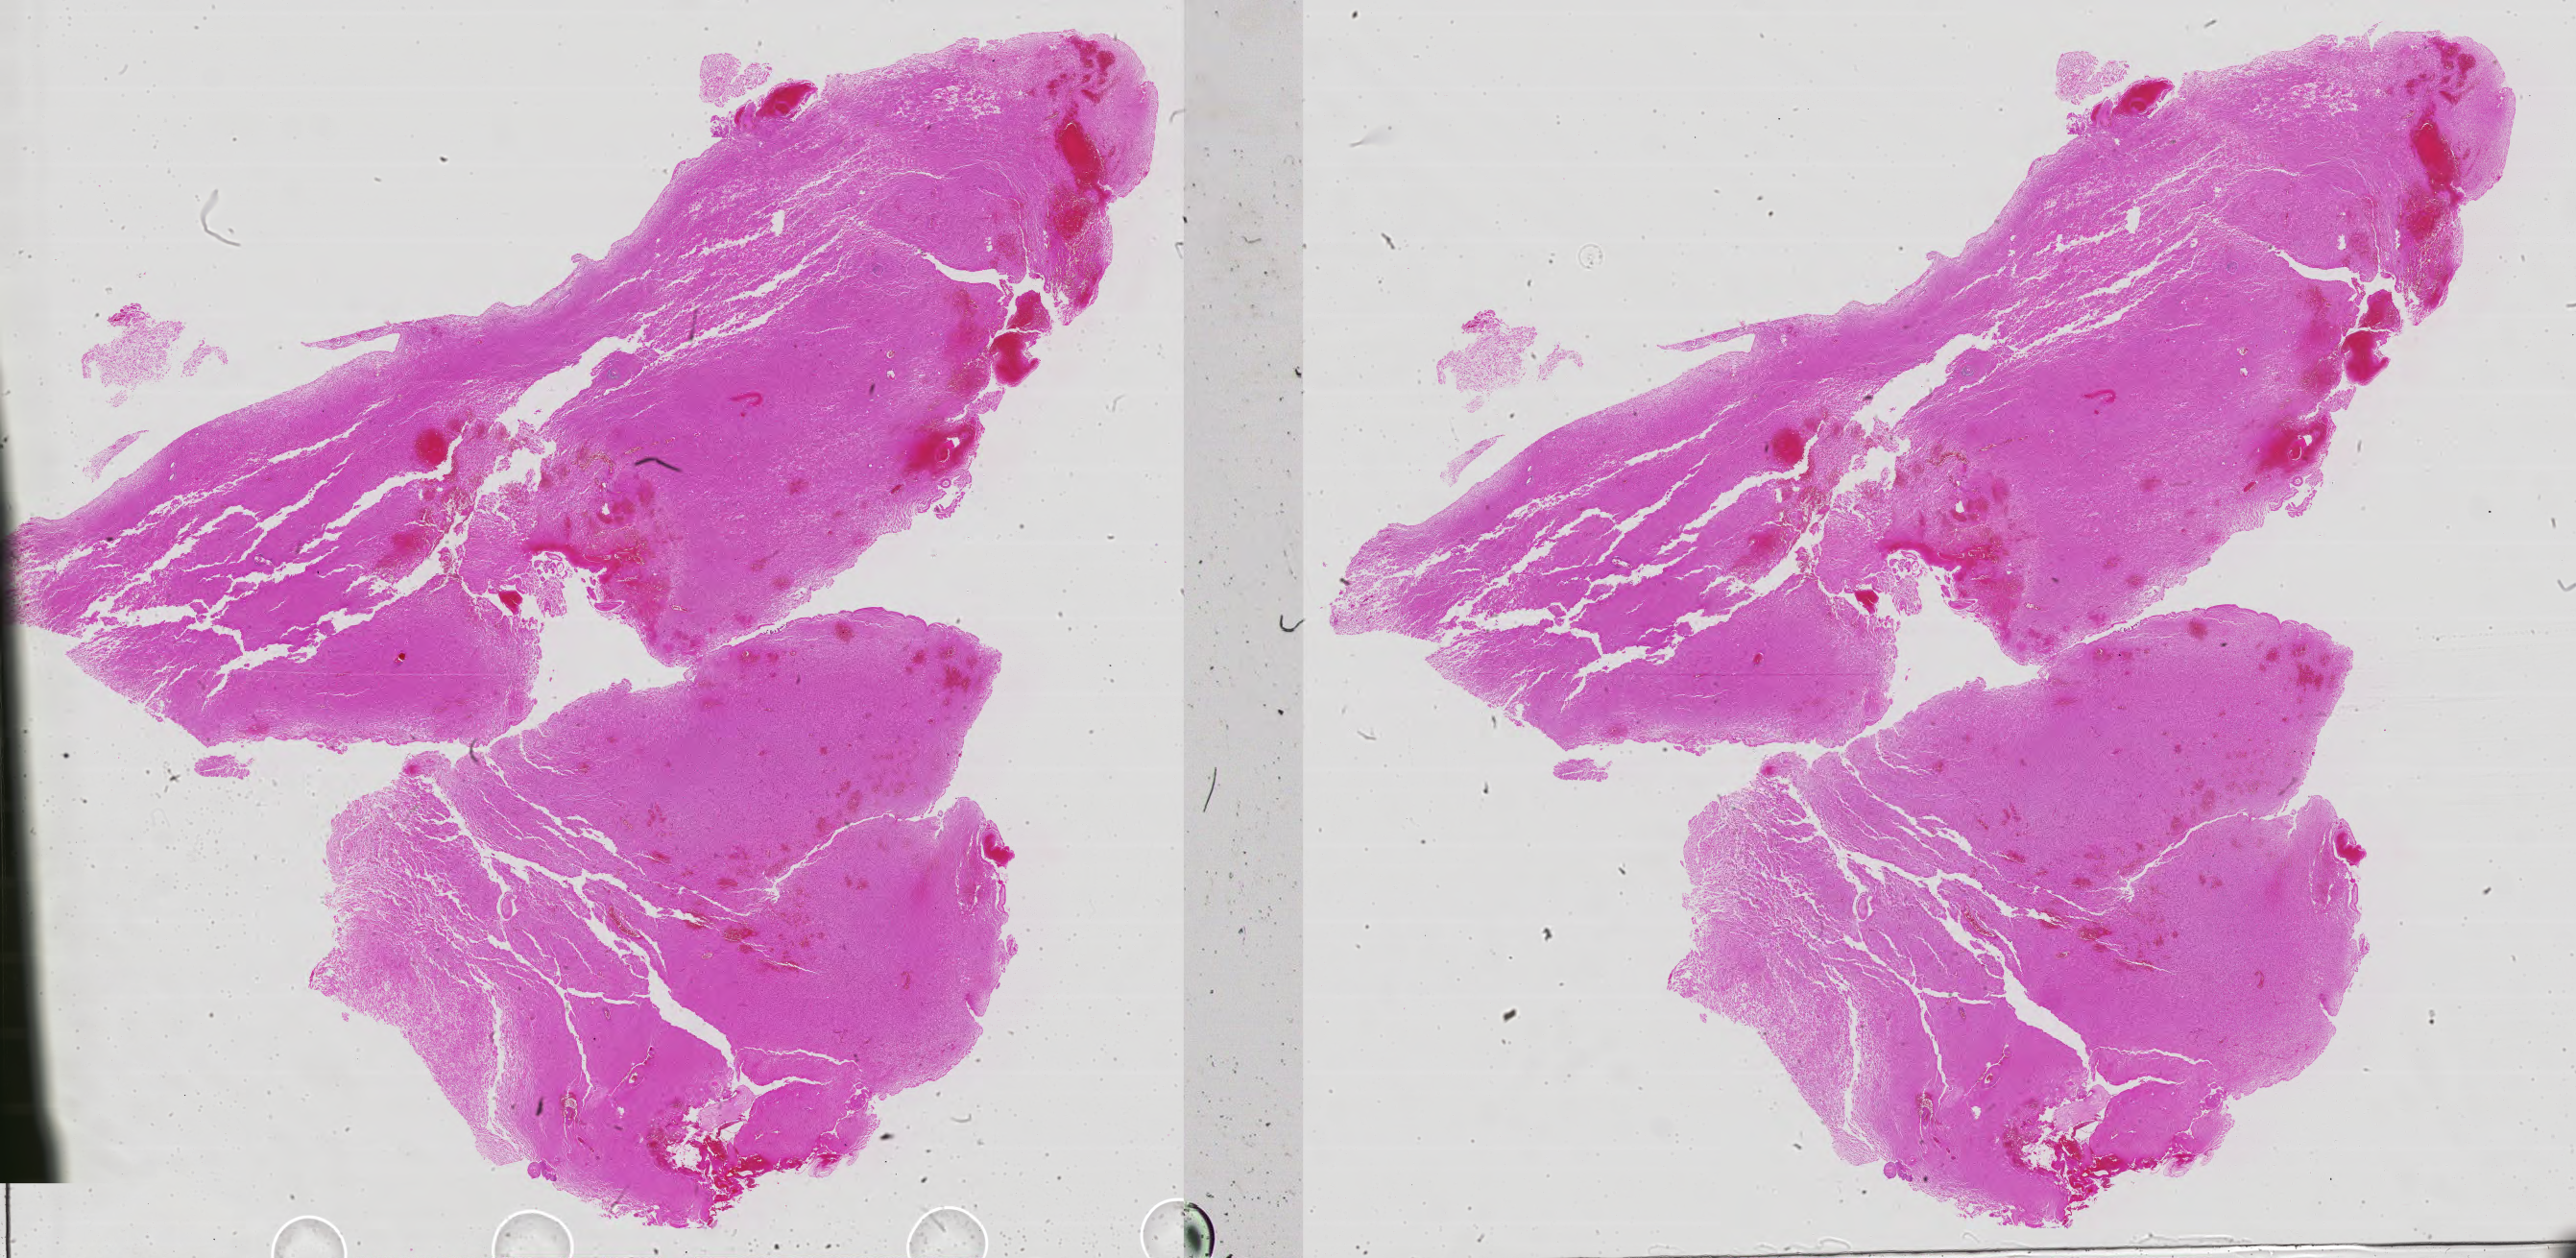
Digitized Hematoxylin and eosin (H&E) stained tissue section (whole slide) — low-resolution overview of the scanned area, about 42.9 x 21.0 mm (acquisition: 40x scan). Formalin-fixed paraffin-embedded (FFPE) diagnostic section. Primary tumour sample from the brain. Male patient; age at initial diagnosis 46 years. Histologic grade: G3 (poorly differentiated).
Histologic diagnosis: Astrocytoma, anaplastic (cerebrum).